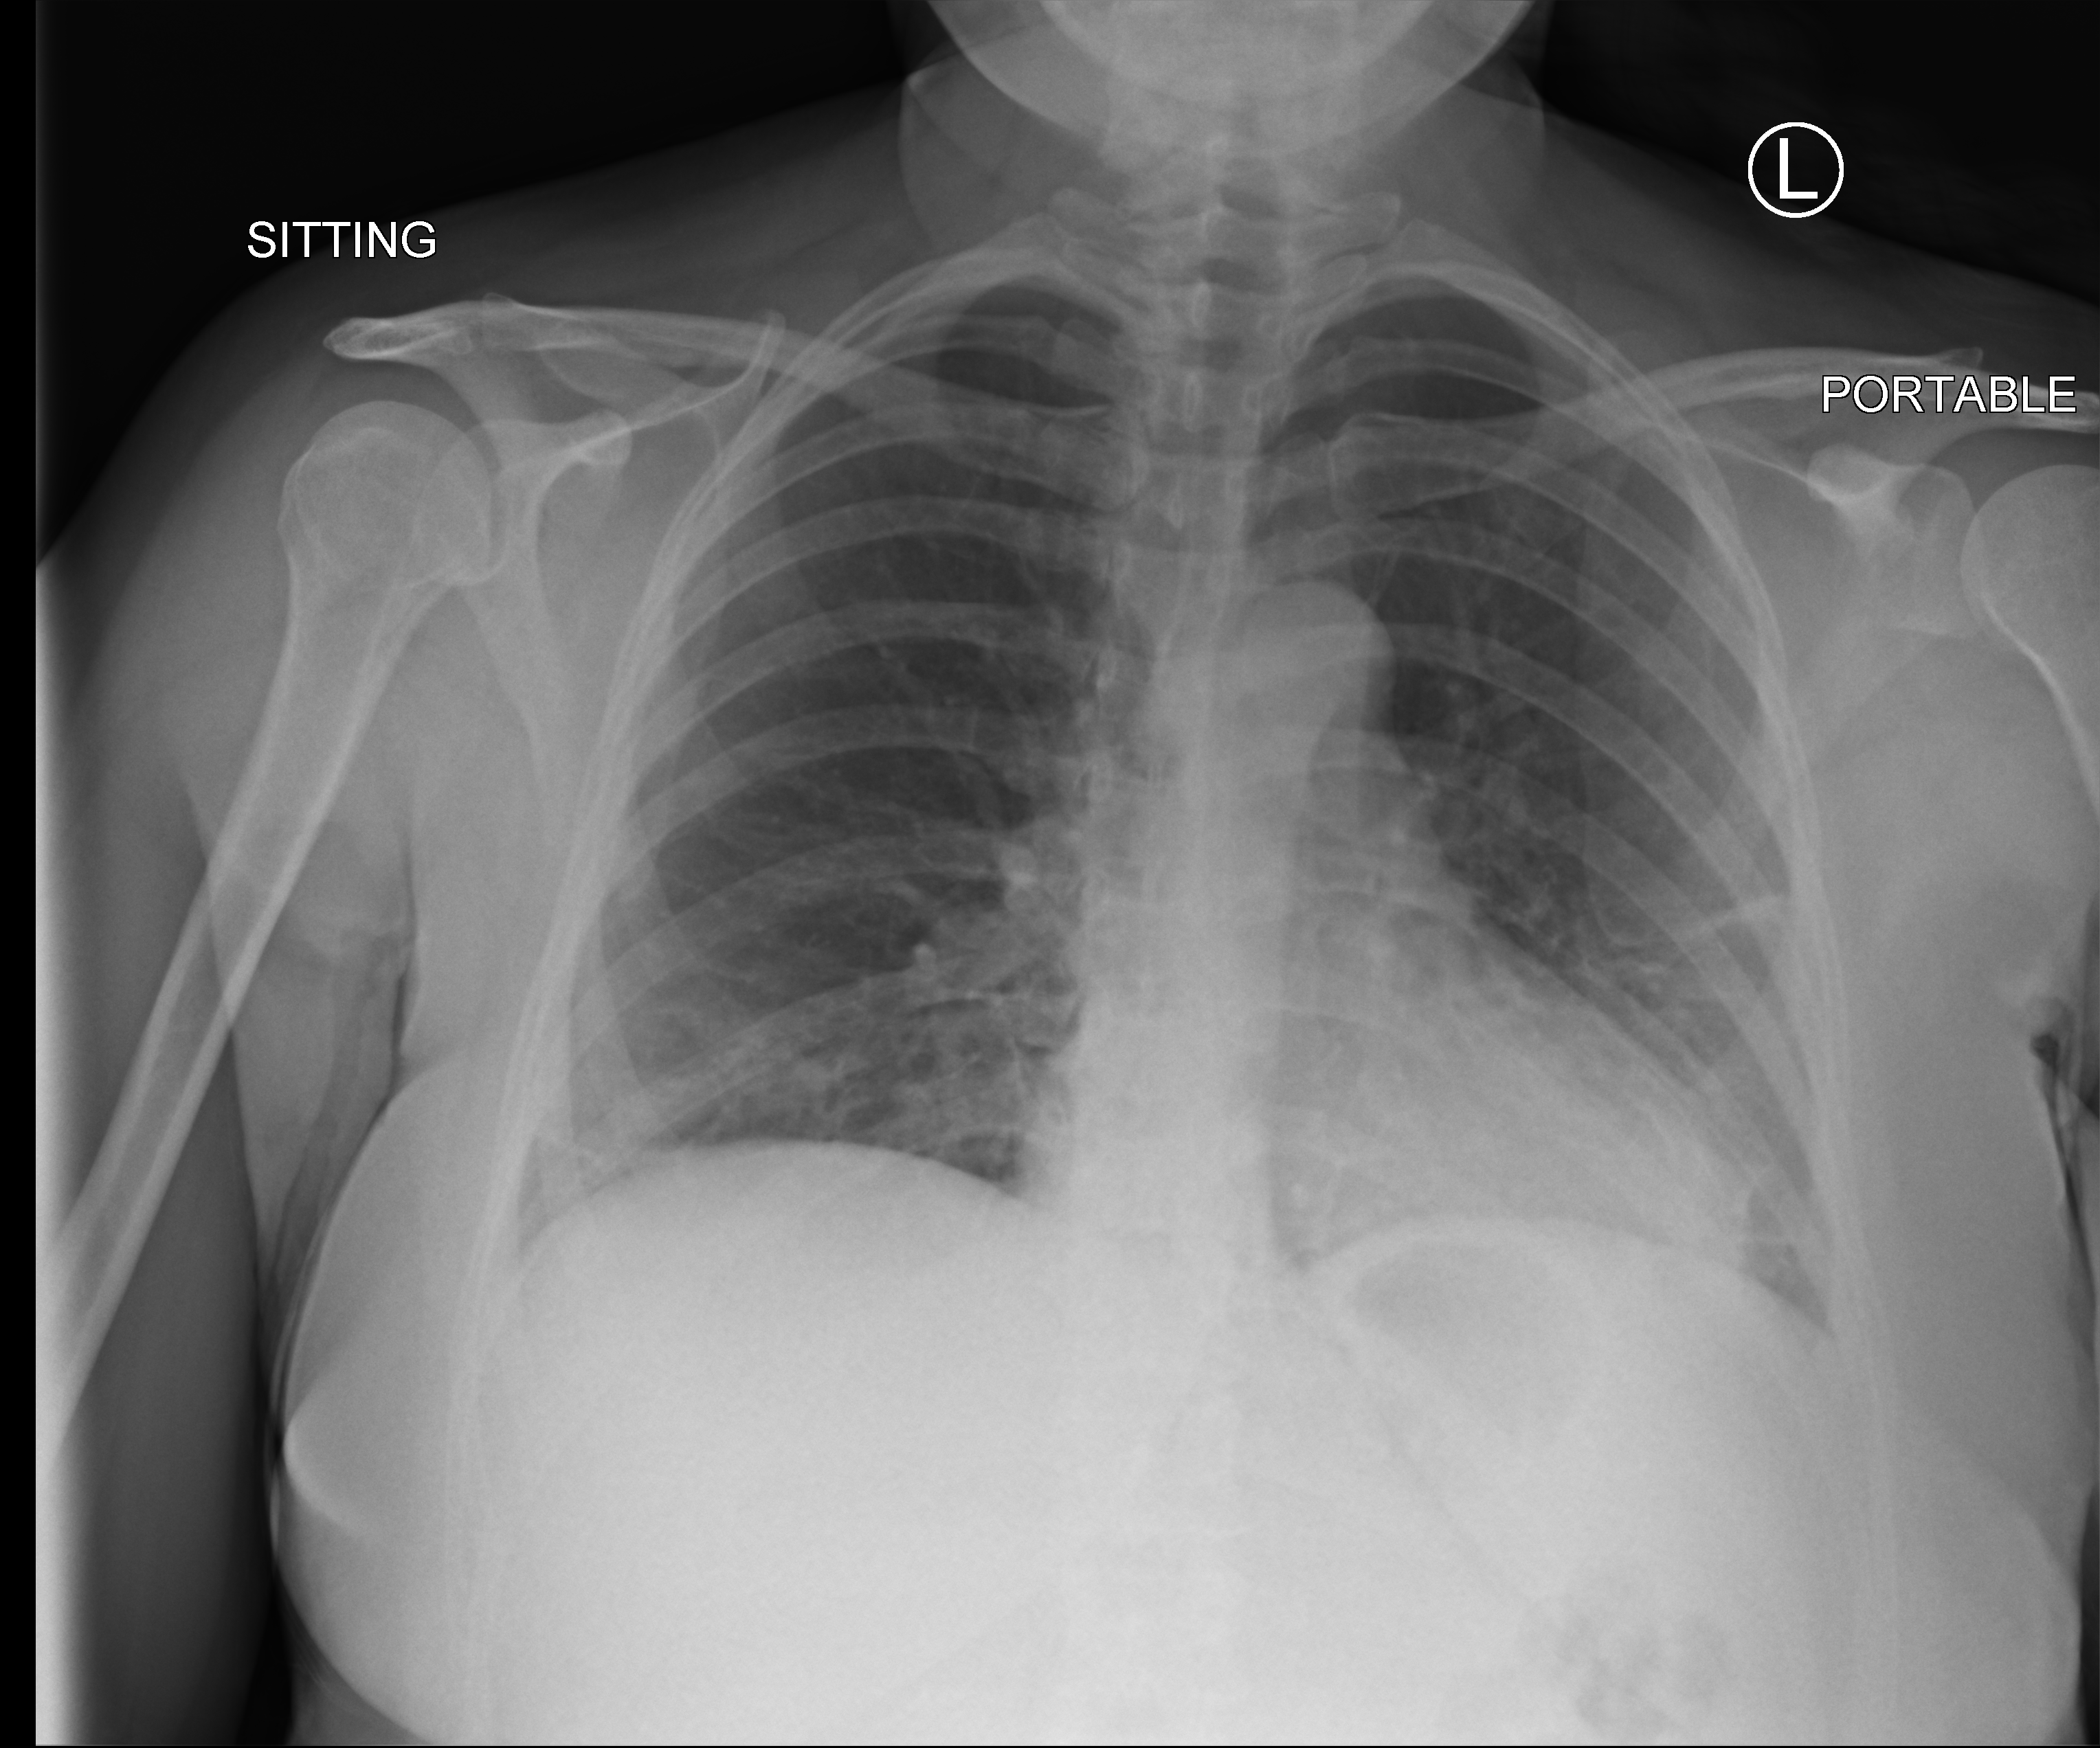
Bedside chest radiograph (computed radiography). Patient hospitalised with COVID-19; female, aged 18–59 years.
Admission-level facts for this patient (not findings on this image; timing relative to this image not recorded): admitted to intensive care during this hospital stay: no; length of hospital stay: 2 days.